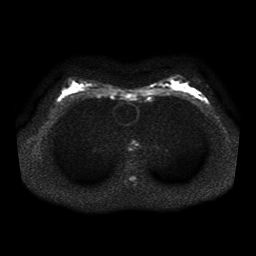
Breast MRI, one axial slice; slice 24 of 41 in the series (ordered by position); diffusion-weighted series; image 2 of 4 stored at this slice position (different b-values; order by instance number); 1.5 T; 5 mm slice thickness; 256 × 256 image matrix. Female patient.
Annotated regions visible in this slice (outlined manually by an expert reader):
- tumour on diffusion-weighted imaging: bounding box (x1, y1, x2, y2) in pixels: (194, 91, 202, 98)